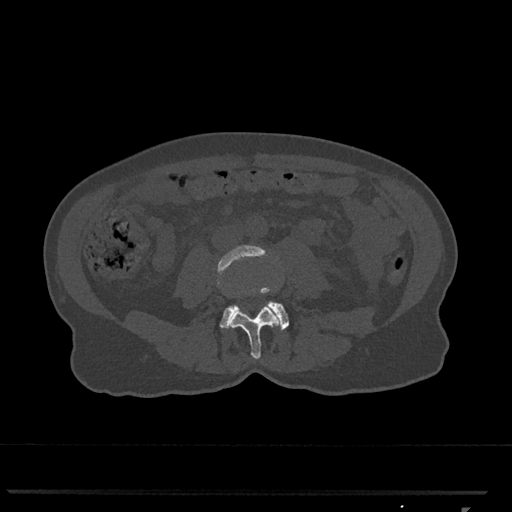
CT including the spine, one axial slice. Reconstruction kernel Br40s/3. Bone window (W 1800 / L 400 HU). 0.5 mm slice thickness. 512 × 512 image matrix. Female patient, age 62 years. From the clinical record (not read from this slice): primary cancer: renal.
Annotated regions visible in this slice (semi-automatic segmentation, software-assisted and operator-edited):
- L3 vertebra: bounding box (x1, y1, x2, y2) in pixels: (217, 245, 282, 359)
- L4 vertebra: (220, 287, 289, 331)